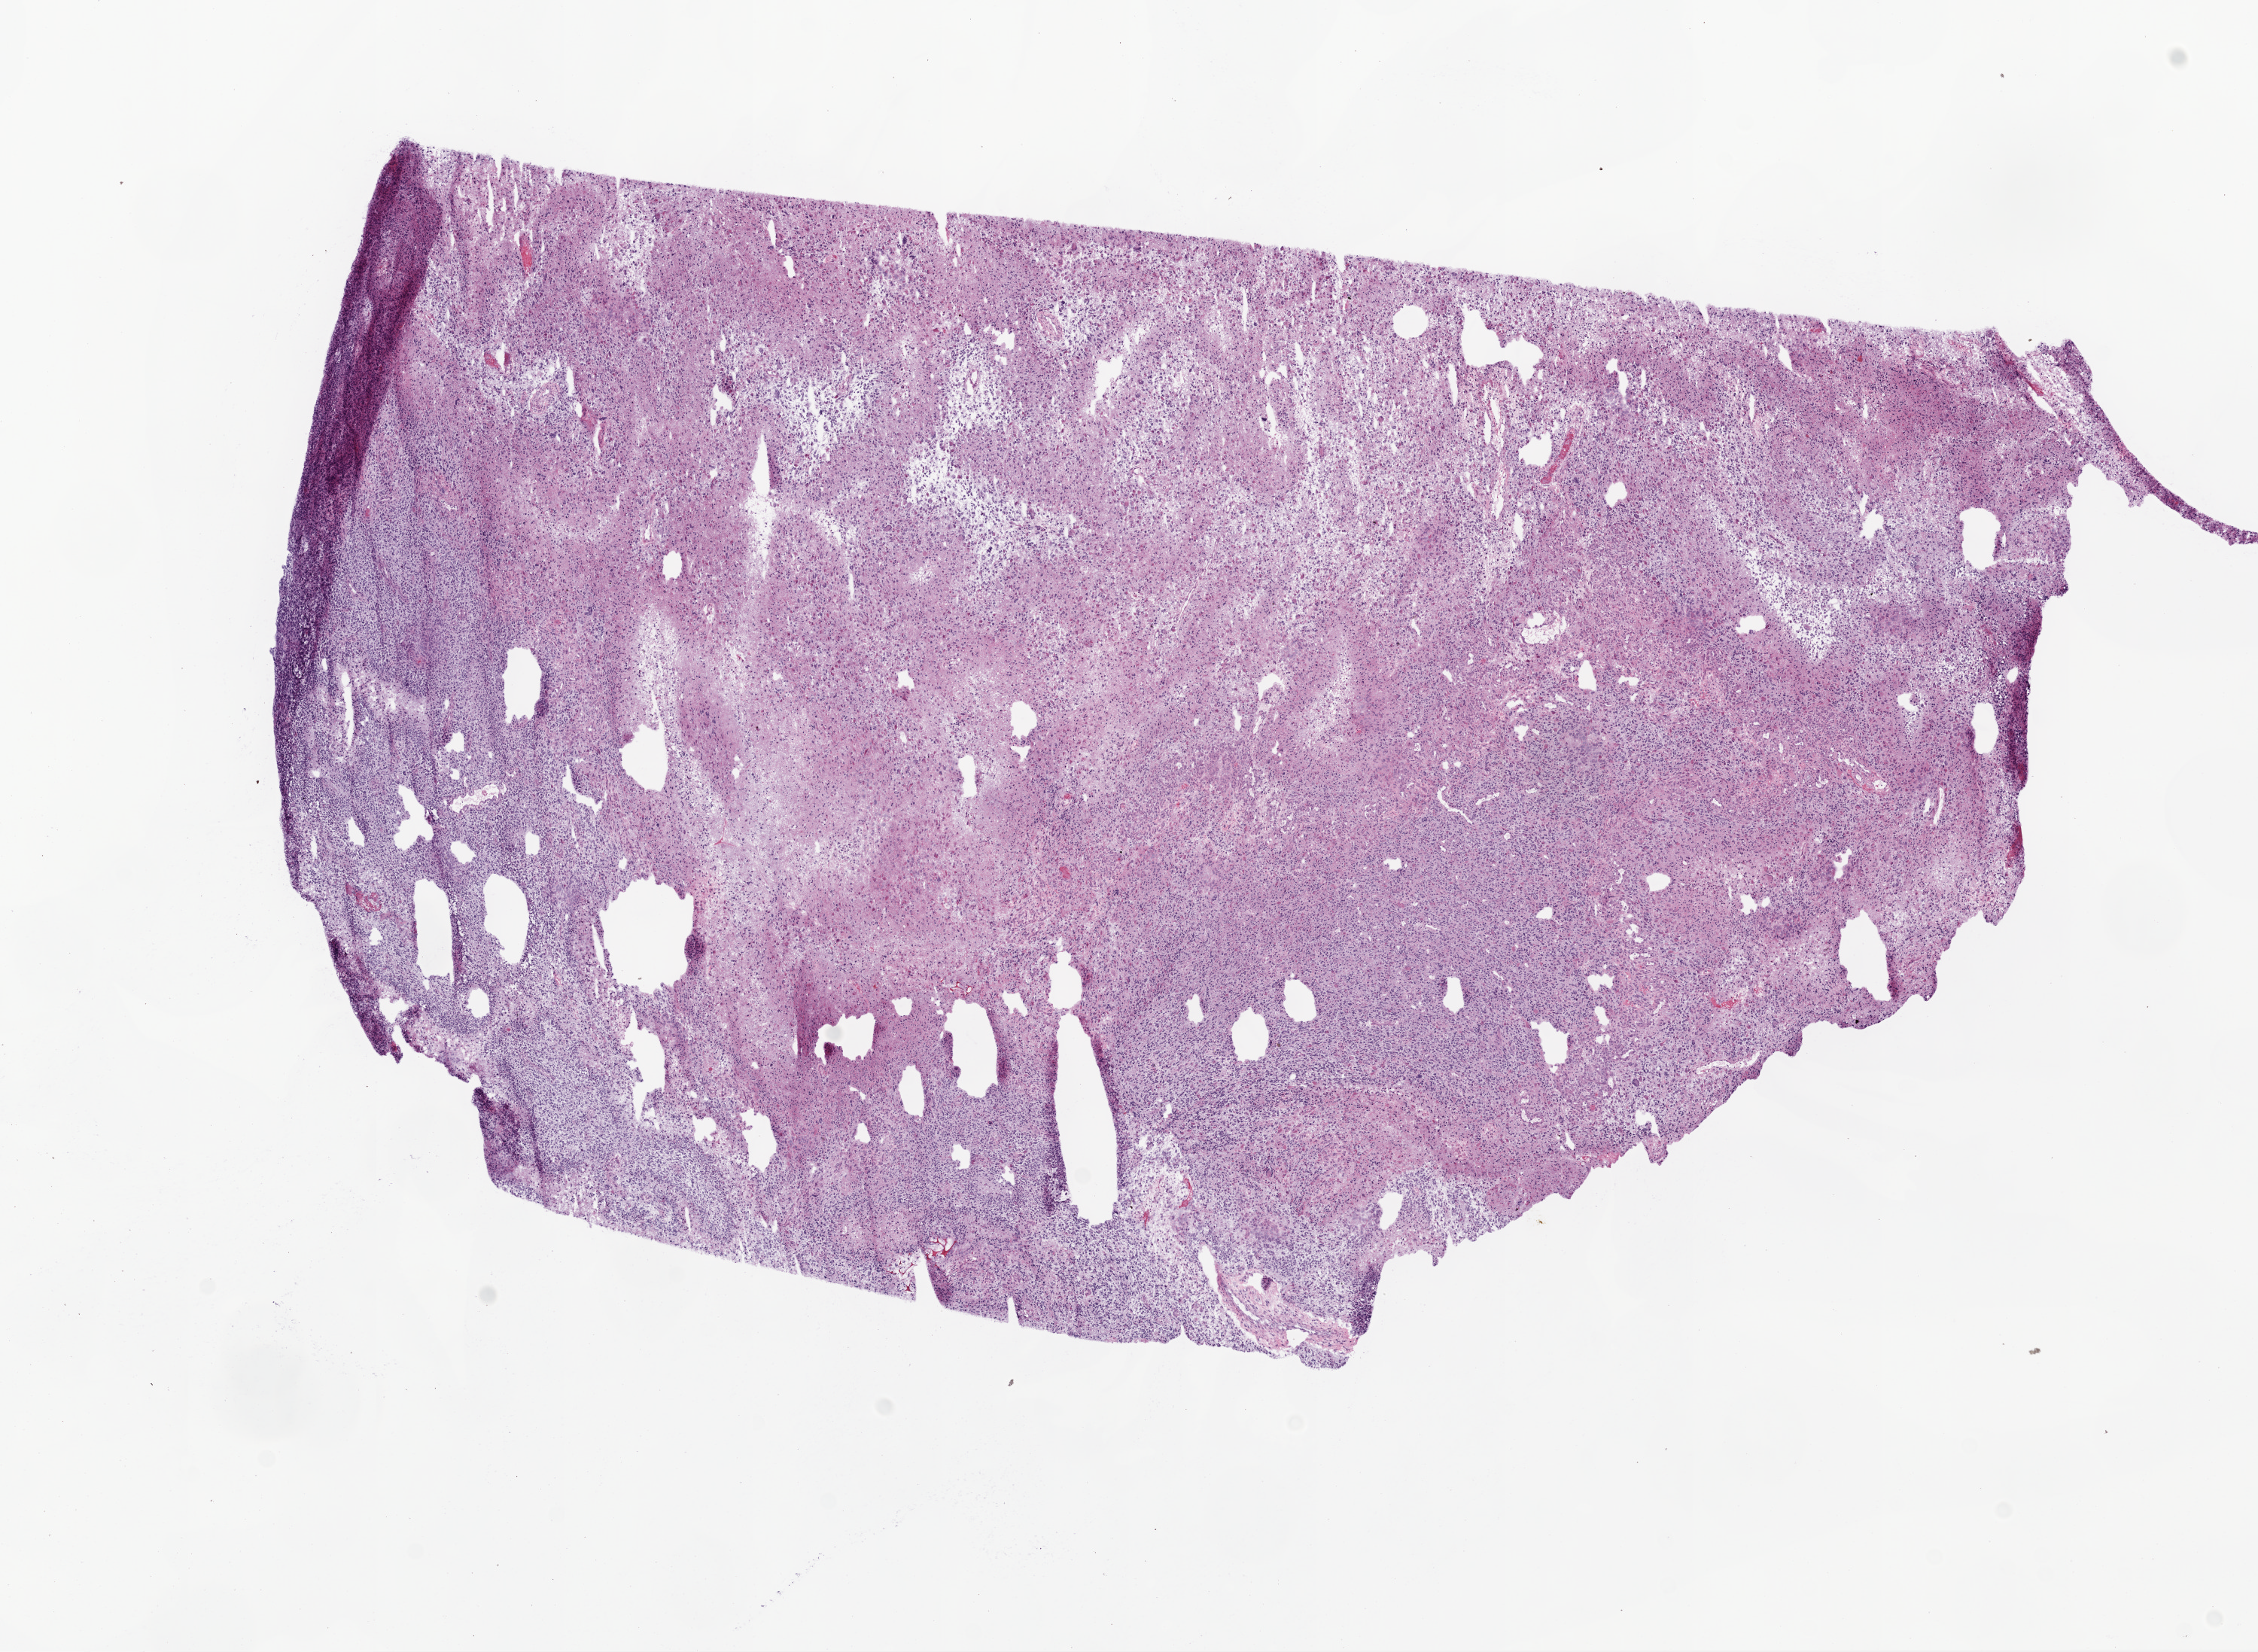
Digitized Hematoxylin and eosin (H&E) stained tissue section (whole slide) — a low-resolution overview of the entire scanned area, about 12.0 x 8.8 mm; frozen section from the top of the tissue portion; sample: primary tumour, brain. Male patient; age at initial diagnosis 83 years. Slide review estimates, as recorded: tumour cells 93%, tumour nuclei 85%, normal cells 0%, stromal cells 0%, necrosis 7%.
Diagnosis: Glioblastoma.